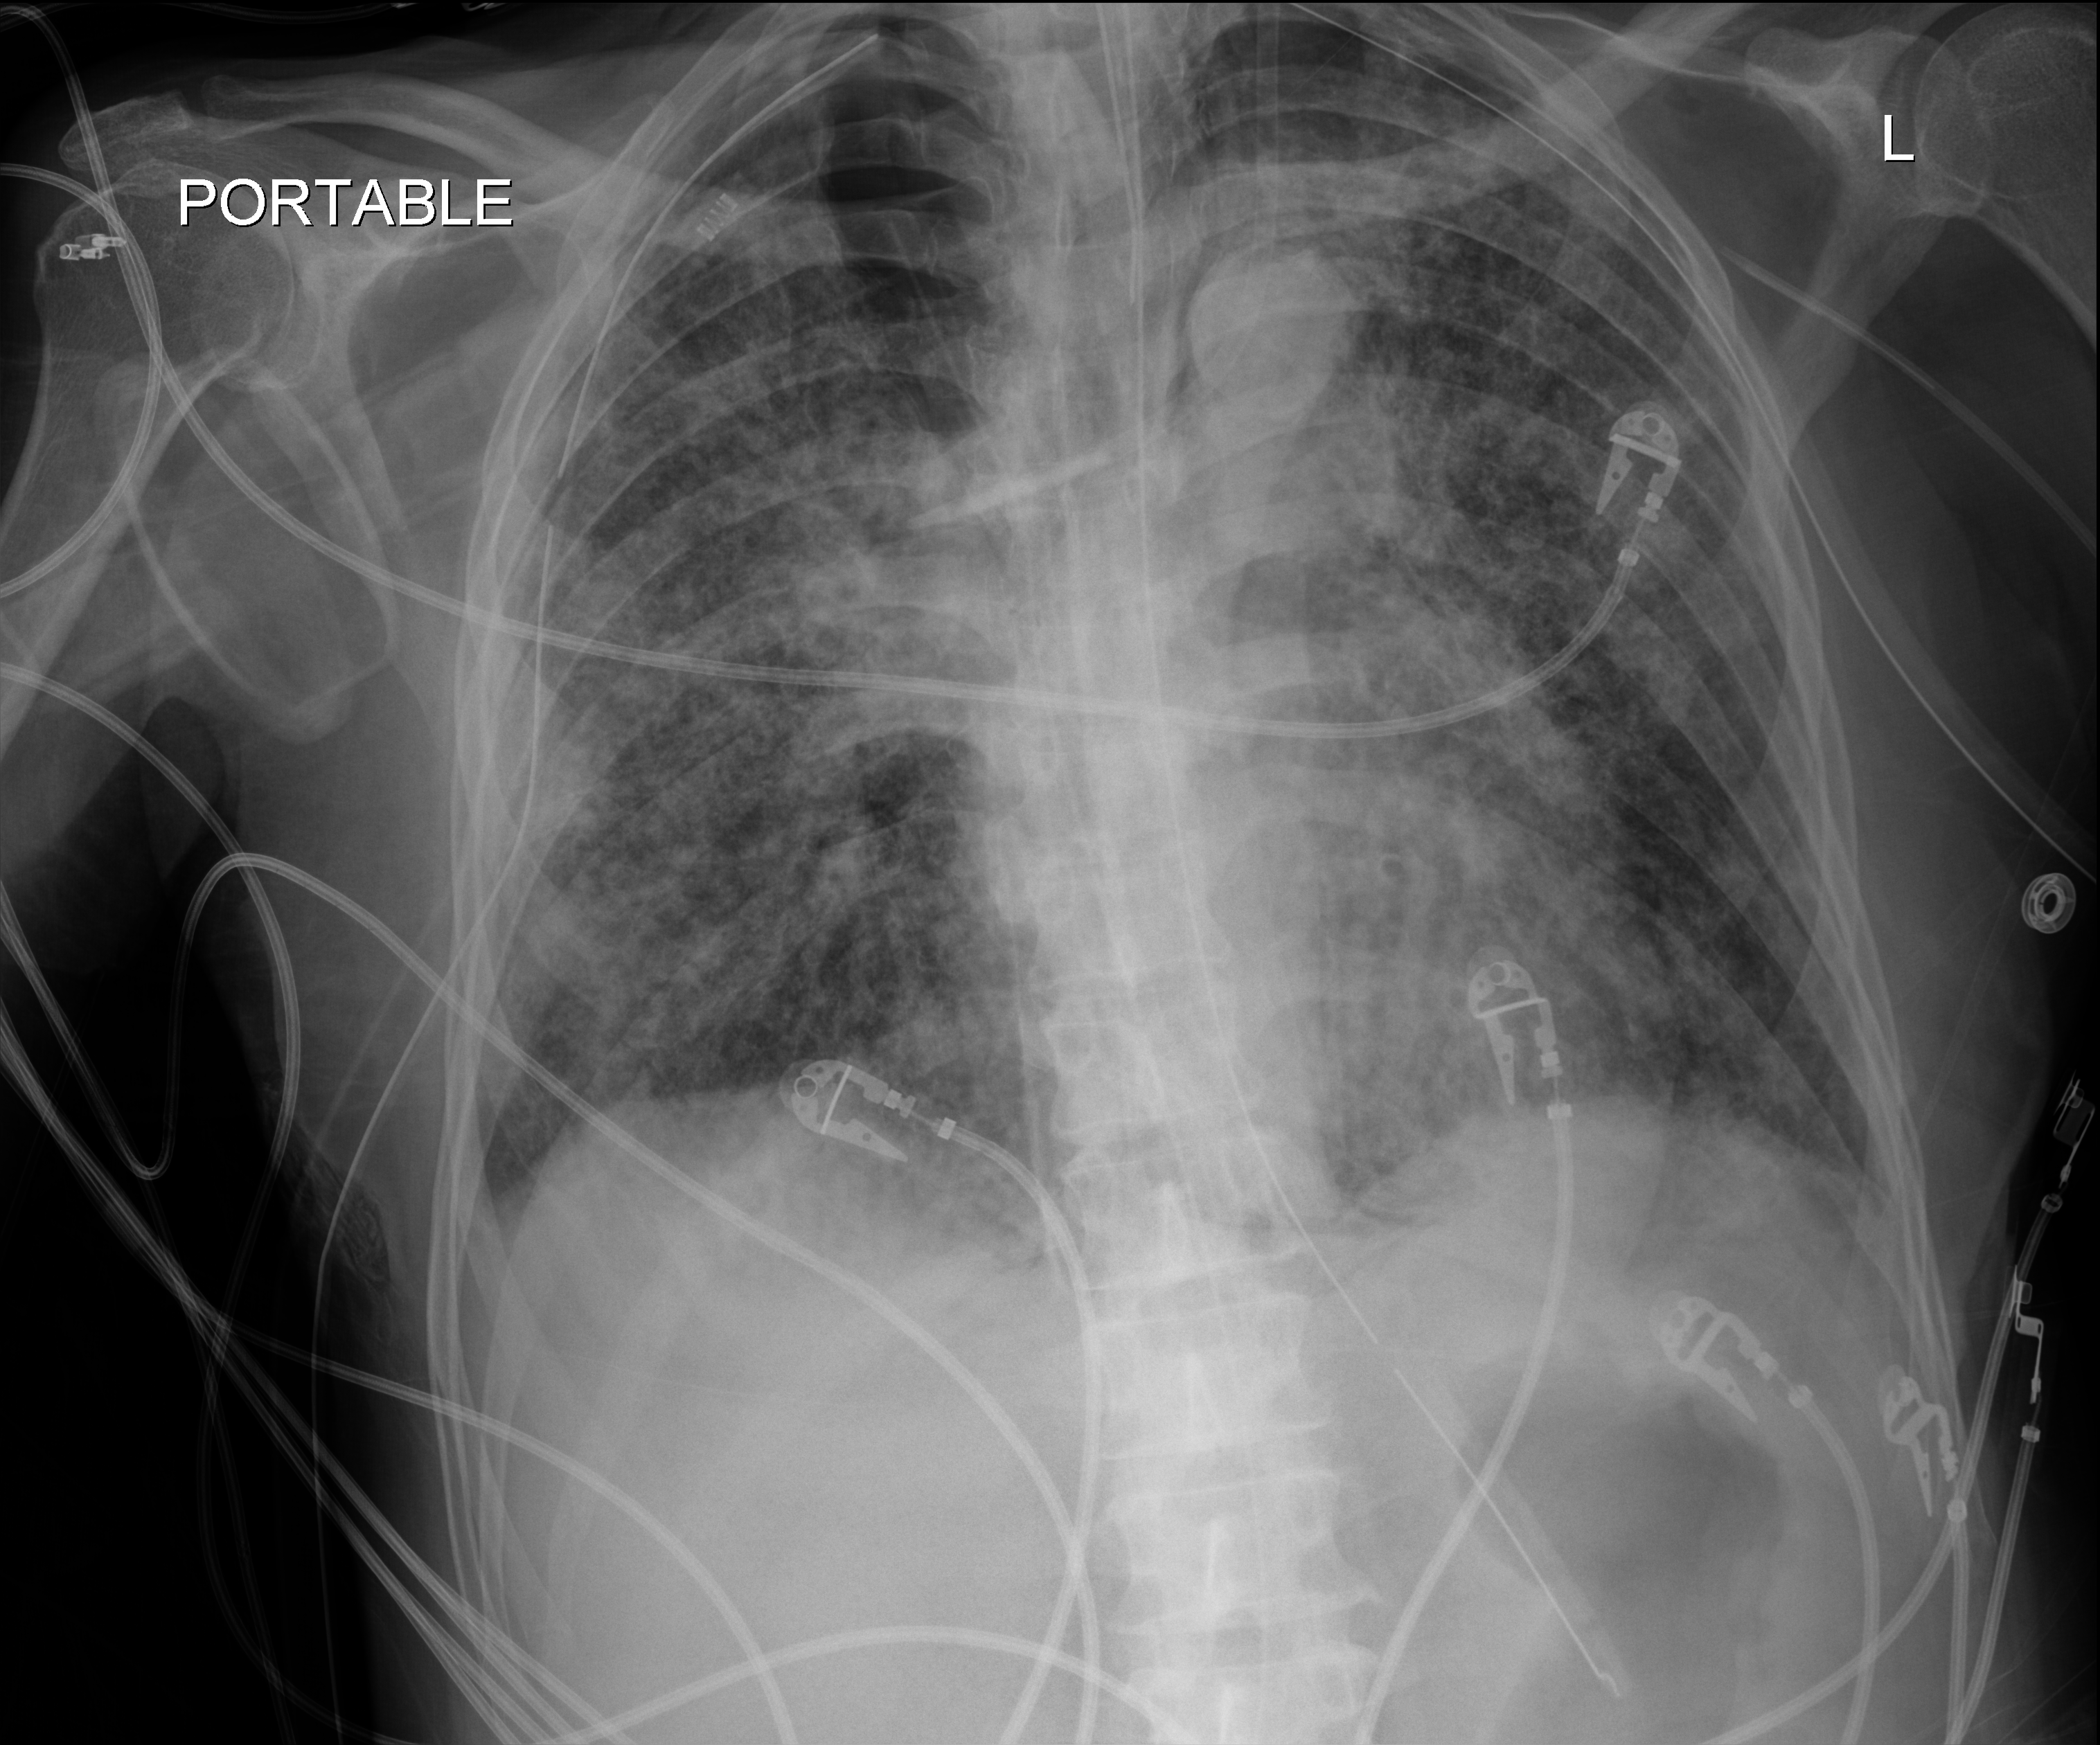
Portable chest radiograph, anteroposterior (AP) projection. Male patient hospitalised with COVID-19, age 60–74 years.
Admission-level facts for this patient (not findings on this image; timing relative to this image not recorded): chronic kidney disease (admission record): no; other chronic lung disease (admission record): yes.